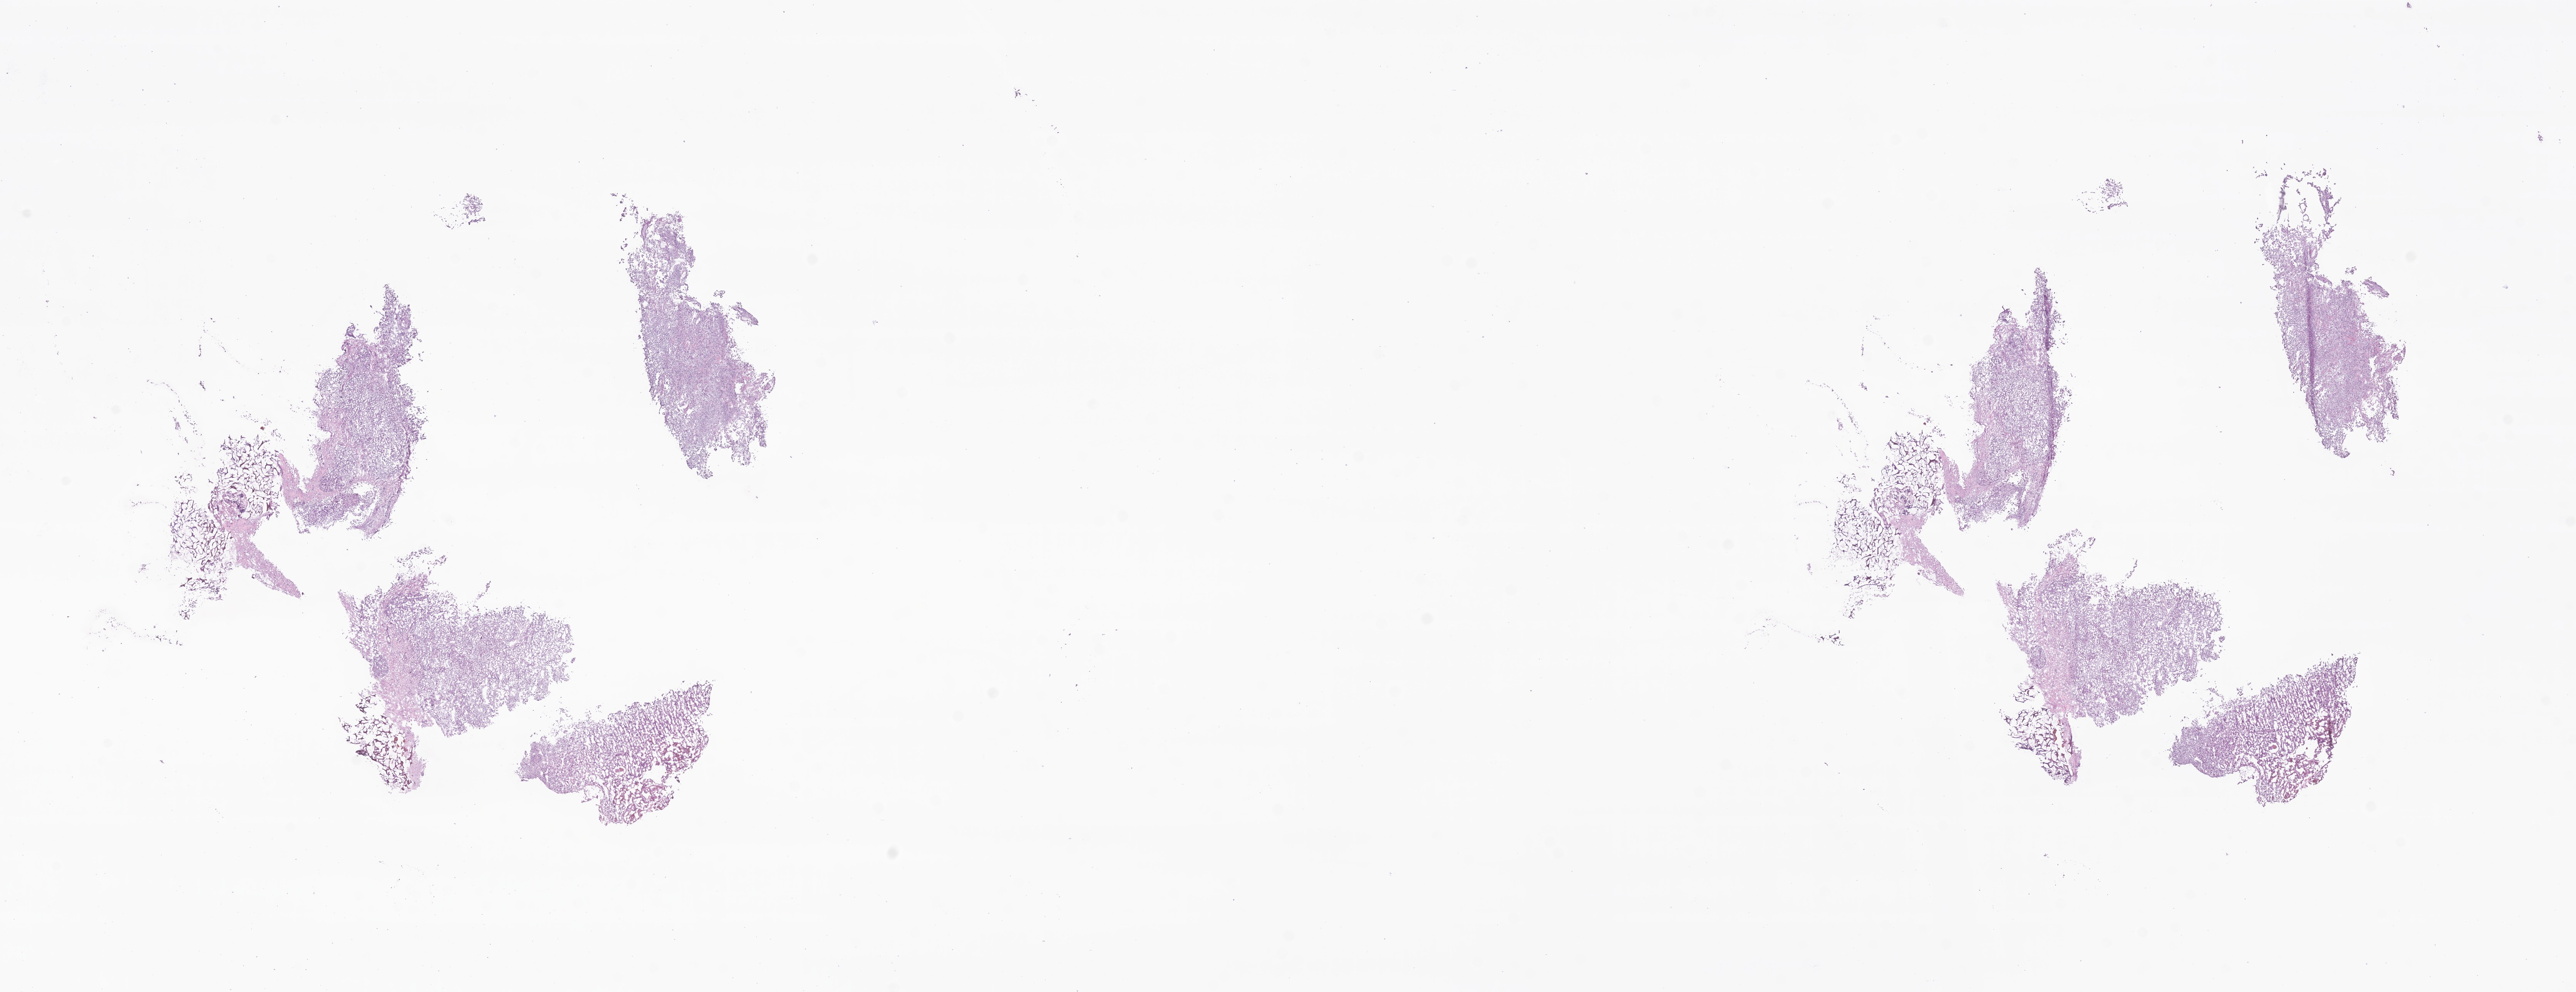
Whole-slide image, H&E stain of tumor tissue from the brain, shown as a low-resolution overview of the whole scanned area (about 28.2 x 10.9 mm). Male patient, age 75 months (6 years 3 months).
* specimen: cryosection (OCT / tissue freezing medium)